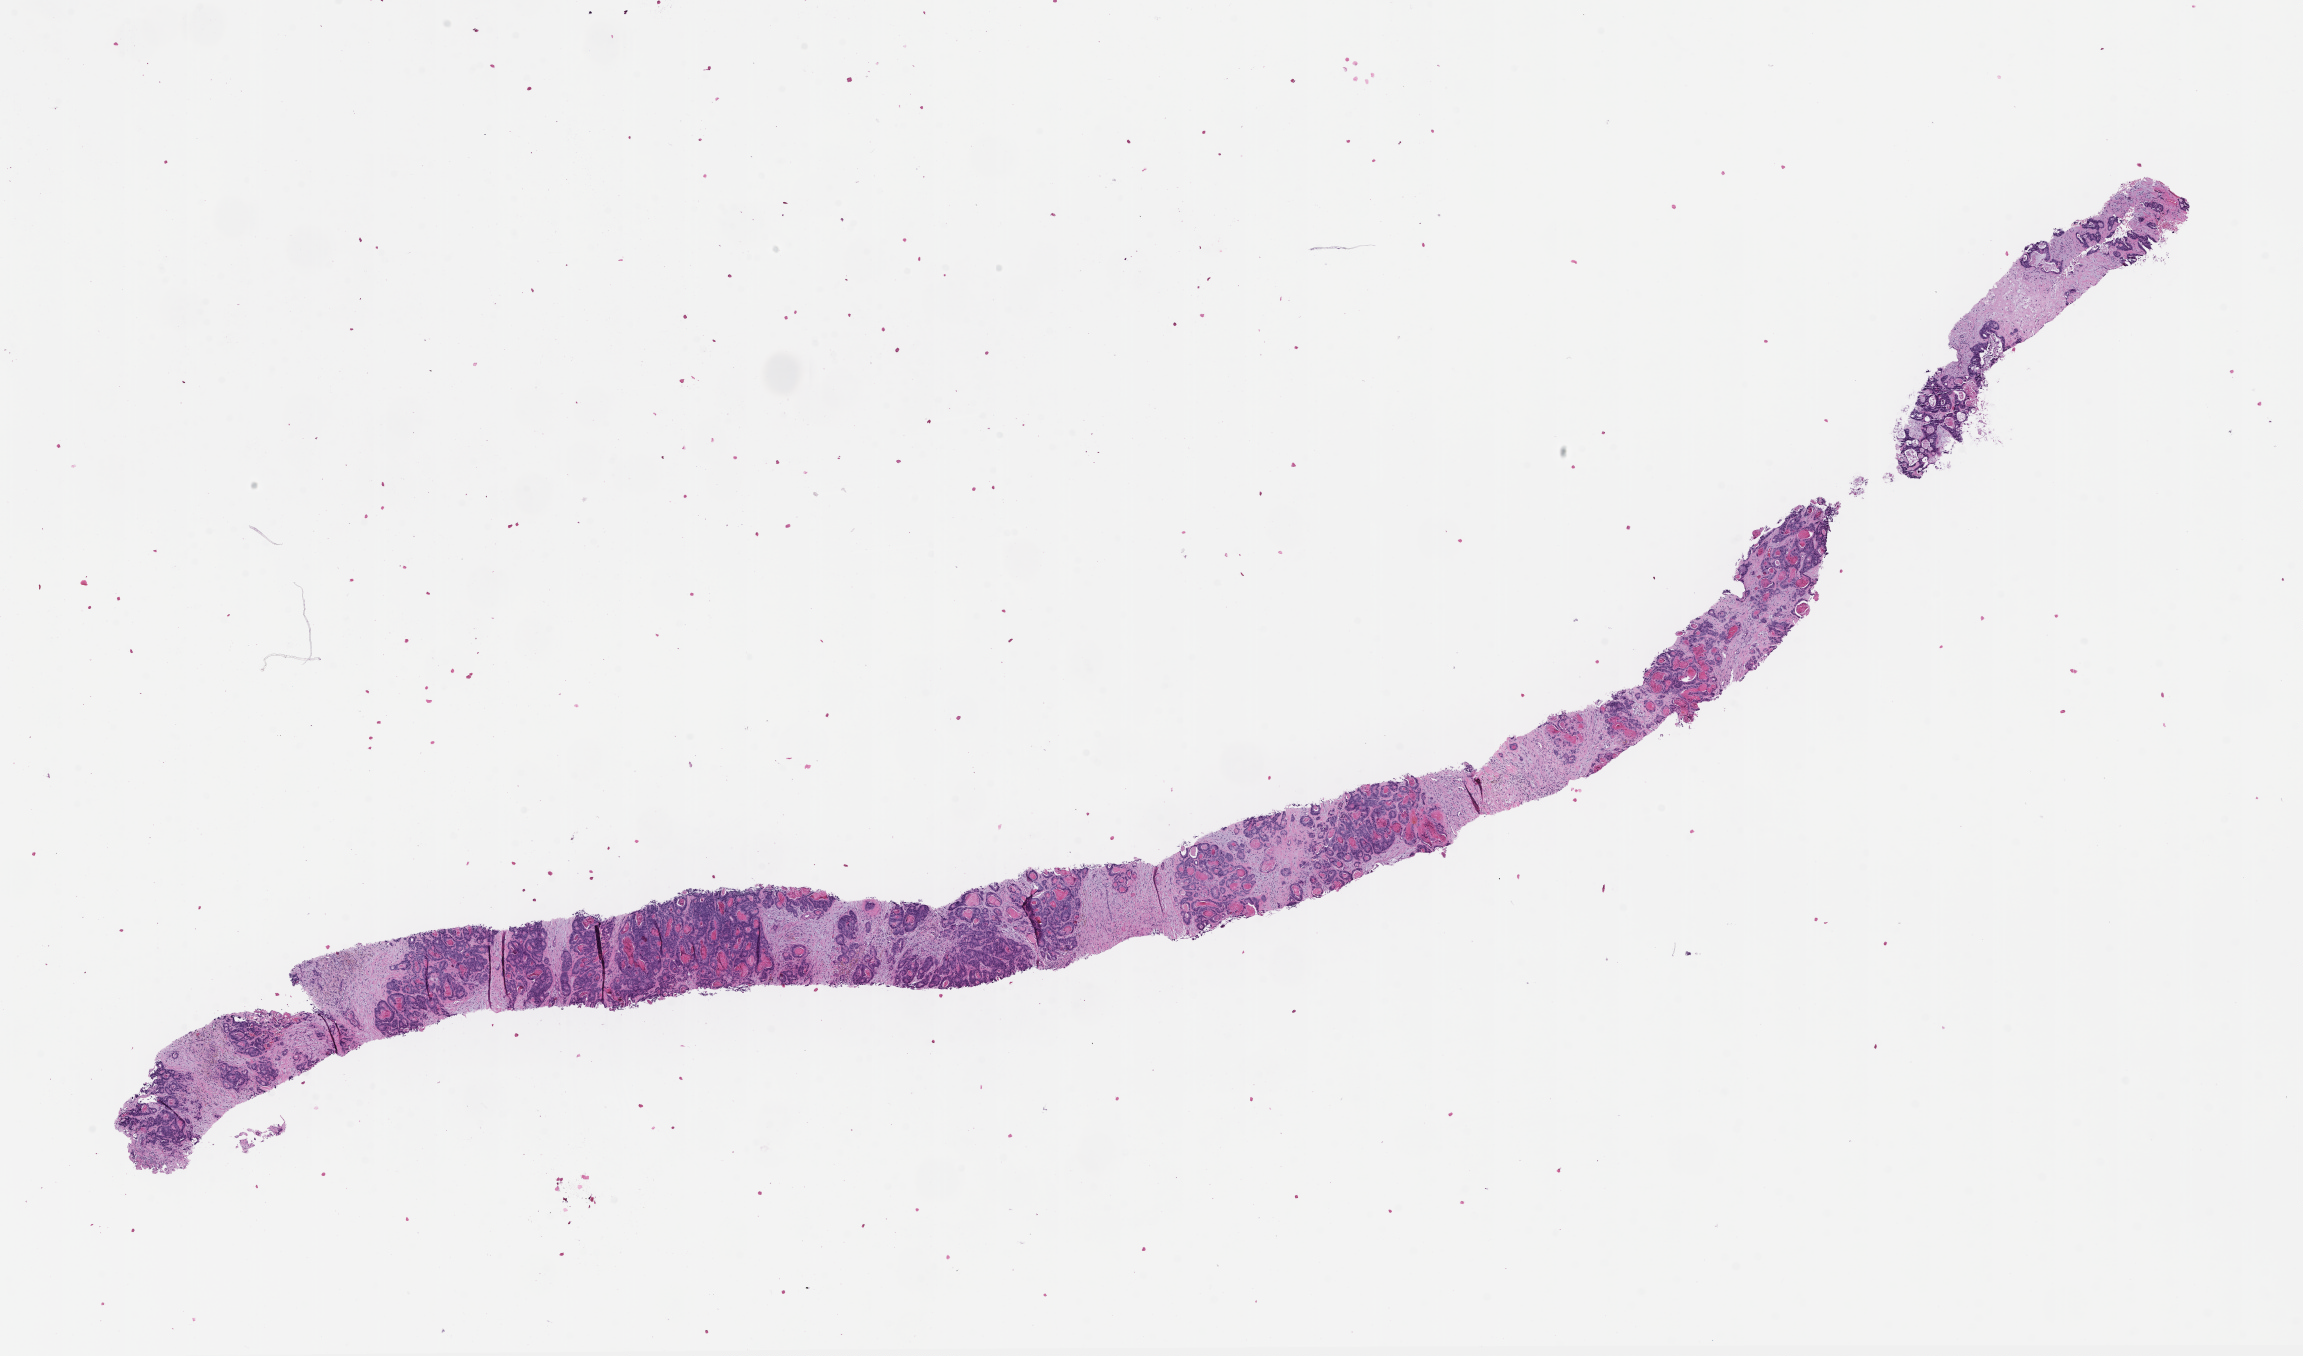
Digitized haematoxylin and eosin-stained section — a low-resolution overview of the entire scanned area, about 18.6 x 10.9 mm, formalin-fixed paraffin-embedded section, collected at disease progression. Patient: male.
This section: metastasis (sampled organ not recorded). Patient diagnosis (primary): Colorectal Carcinoma.